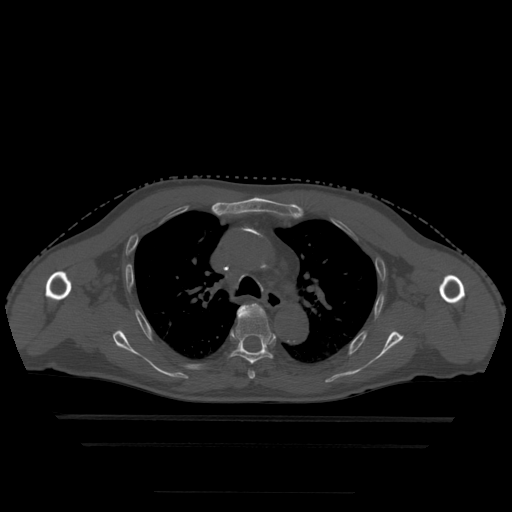
CT including the spine, one axial slice. Position 339 of 522 along the scan axis. Bone window (W 1800 / L 400 HU). 1.25 mm slice thickness. 512 × 512 image matrix, field of view 436 × 436 mm. Patient age 68 years. From the clinical record (not read from this slice): primary cancer: urothelial.
Annotated regions visible in this slice (semi-automatically segmented with operator editing):
- T4 vertebra: bounding box [x1, y1, x2, y2] px = [242, 304, 258, 379]
- T5 vertebra: [232, 306, 274, 365]